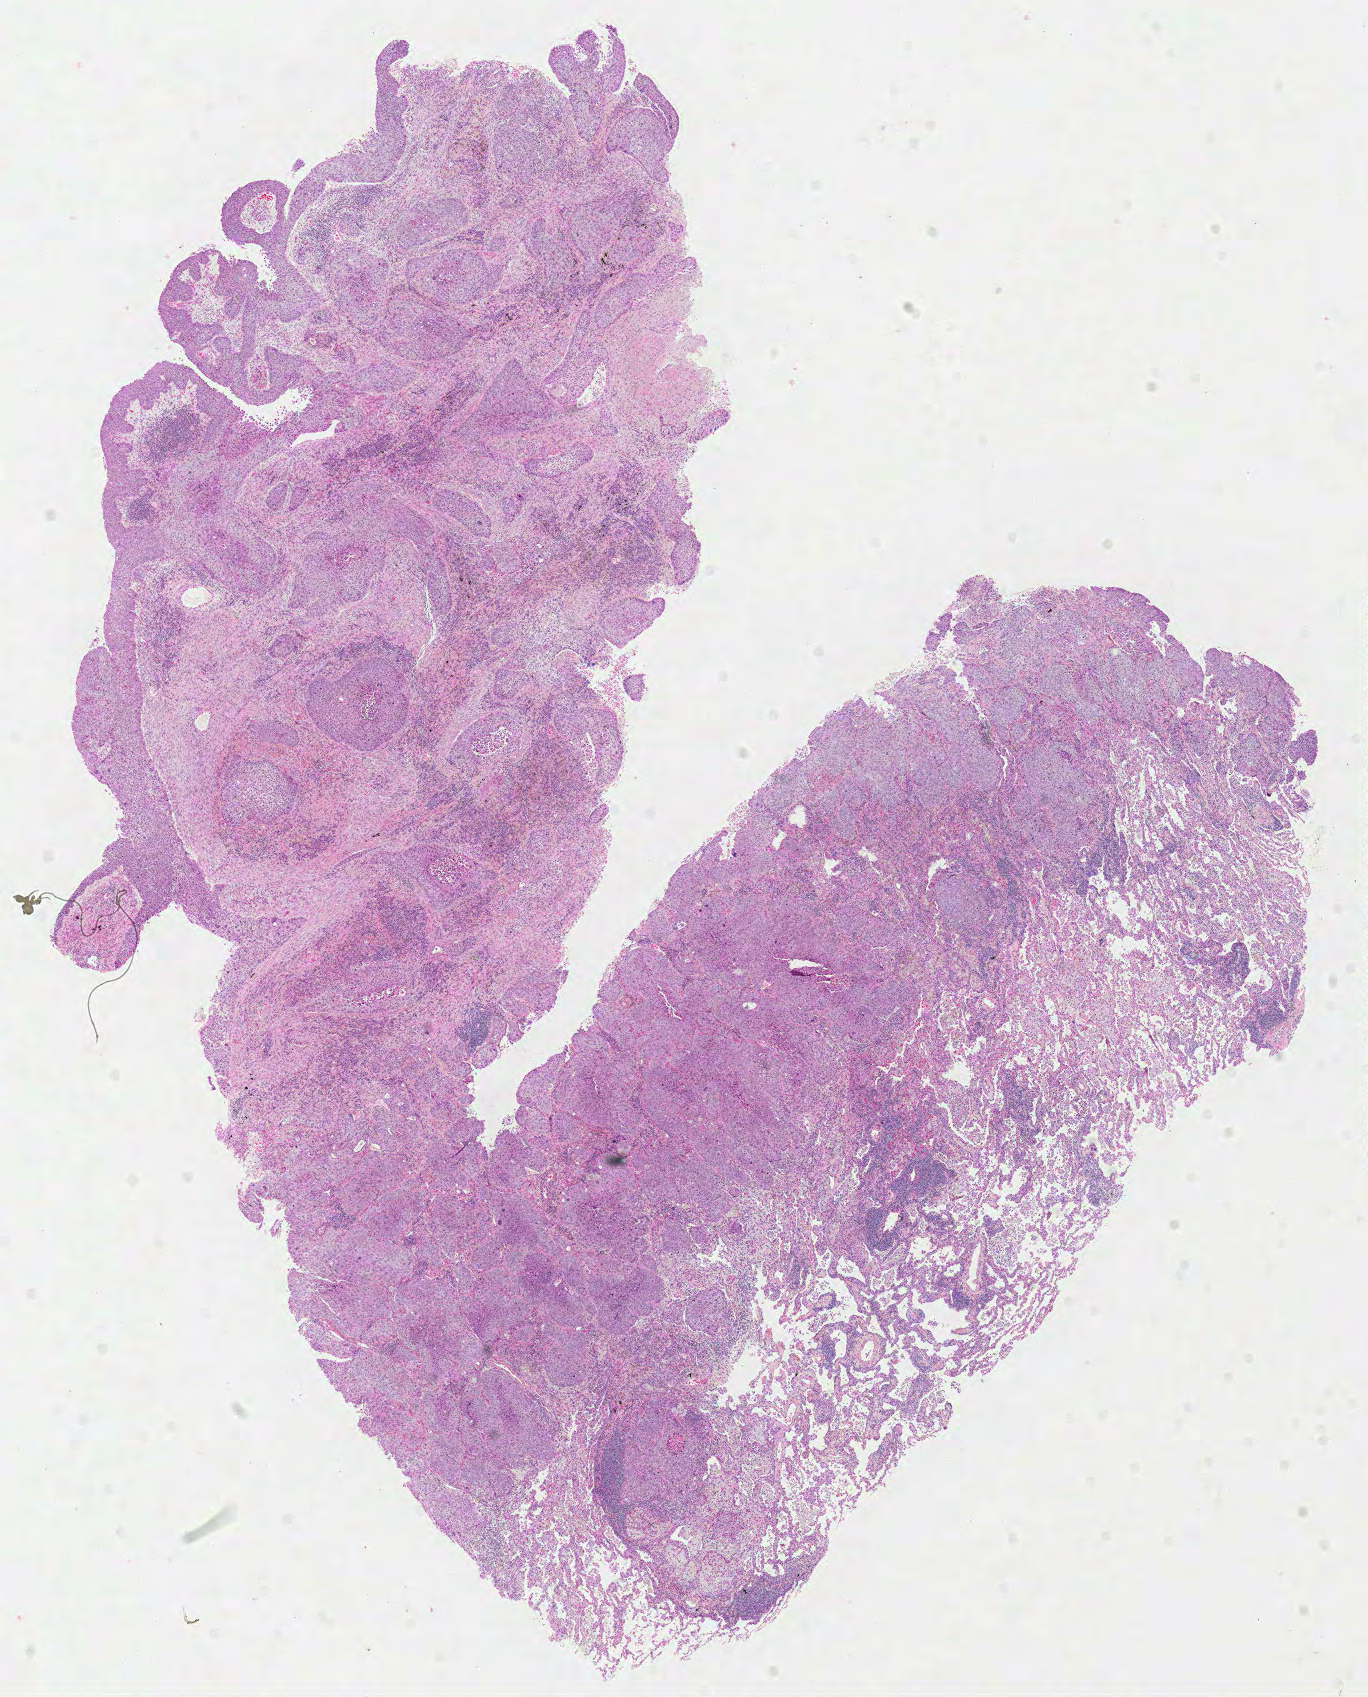
Whole-slide histology image, H&E — low-resolution overview of the scanned area, about 10.8 x 13.4 mm; FFPE section; sample: primary tumour, lung. Female patient; age at initial diagnosis 63 years.
• histologic diagnosis: Squamous cell carcinoma, NOS (upper lobe, lung)
• laterality: left
• AJCC pathologic stage: IB (6th edition)